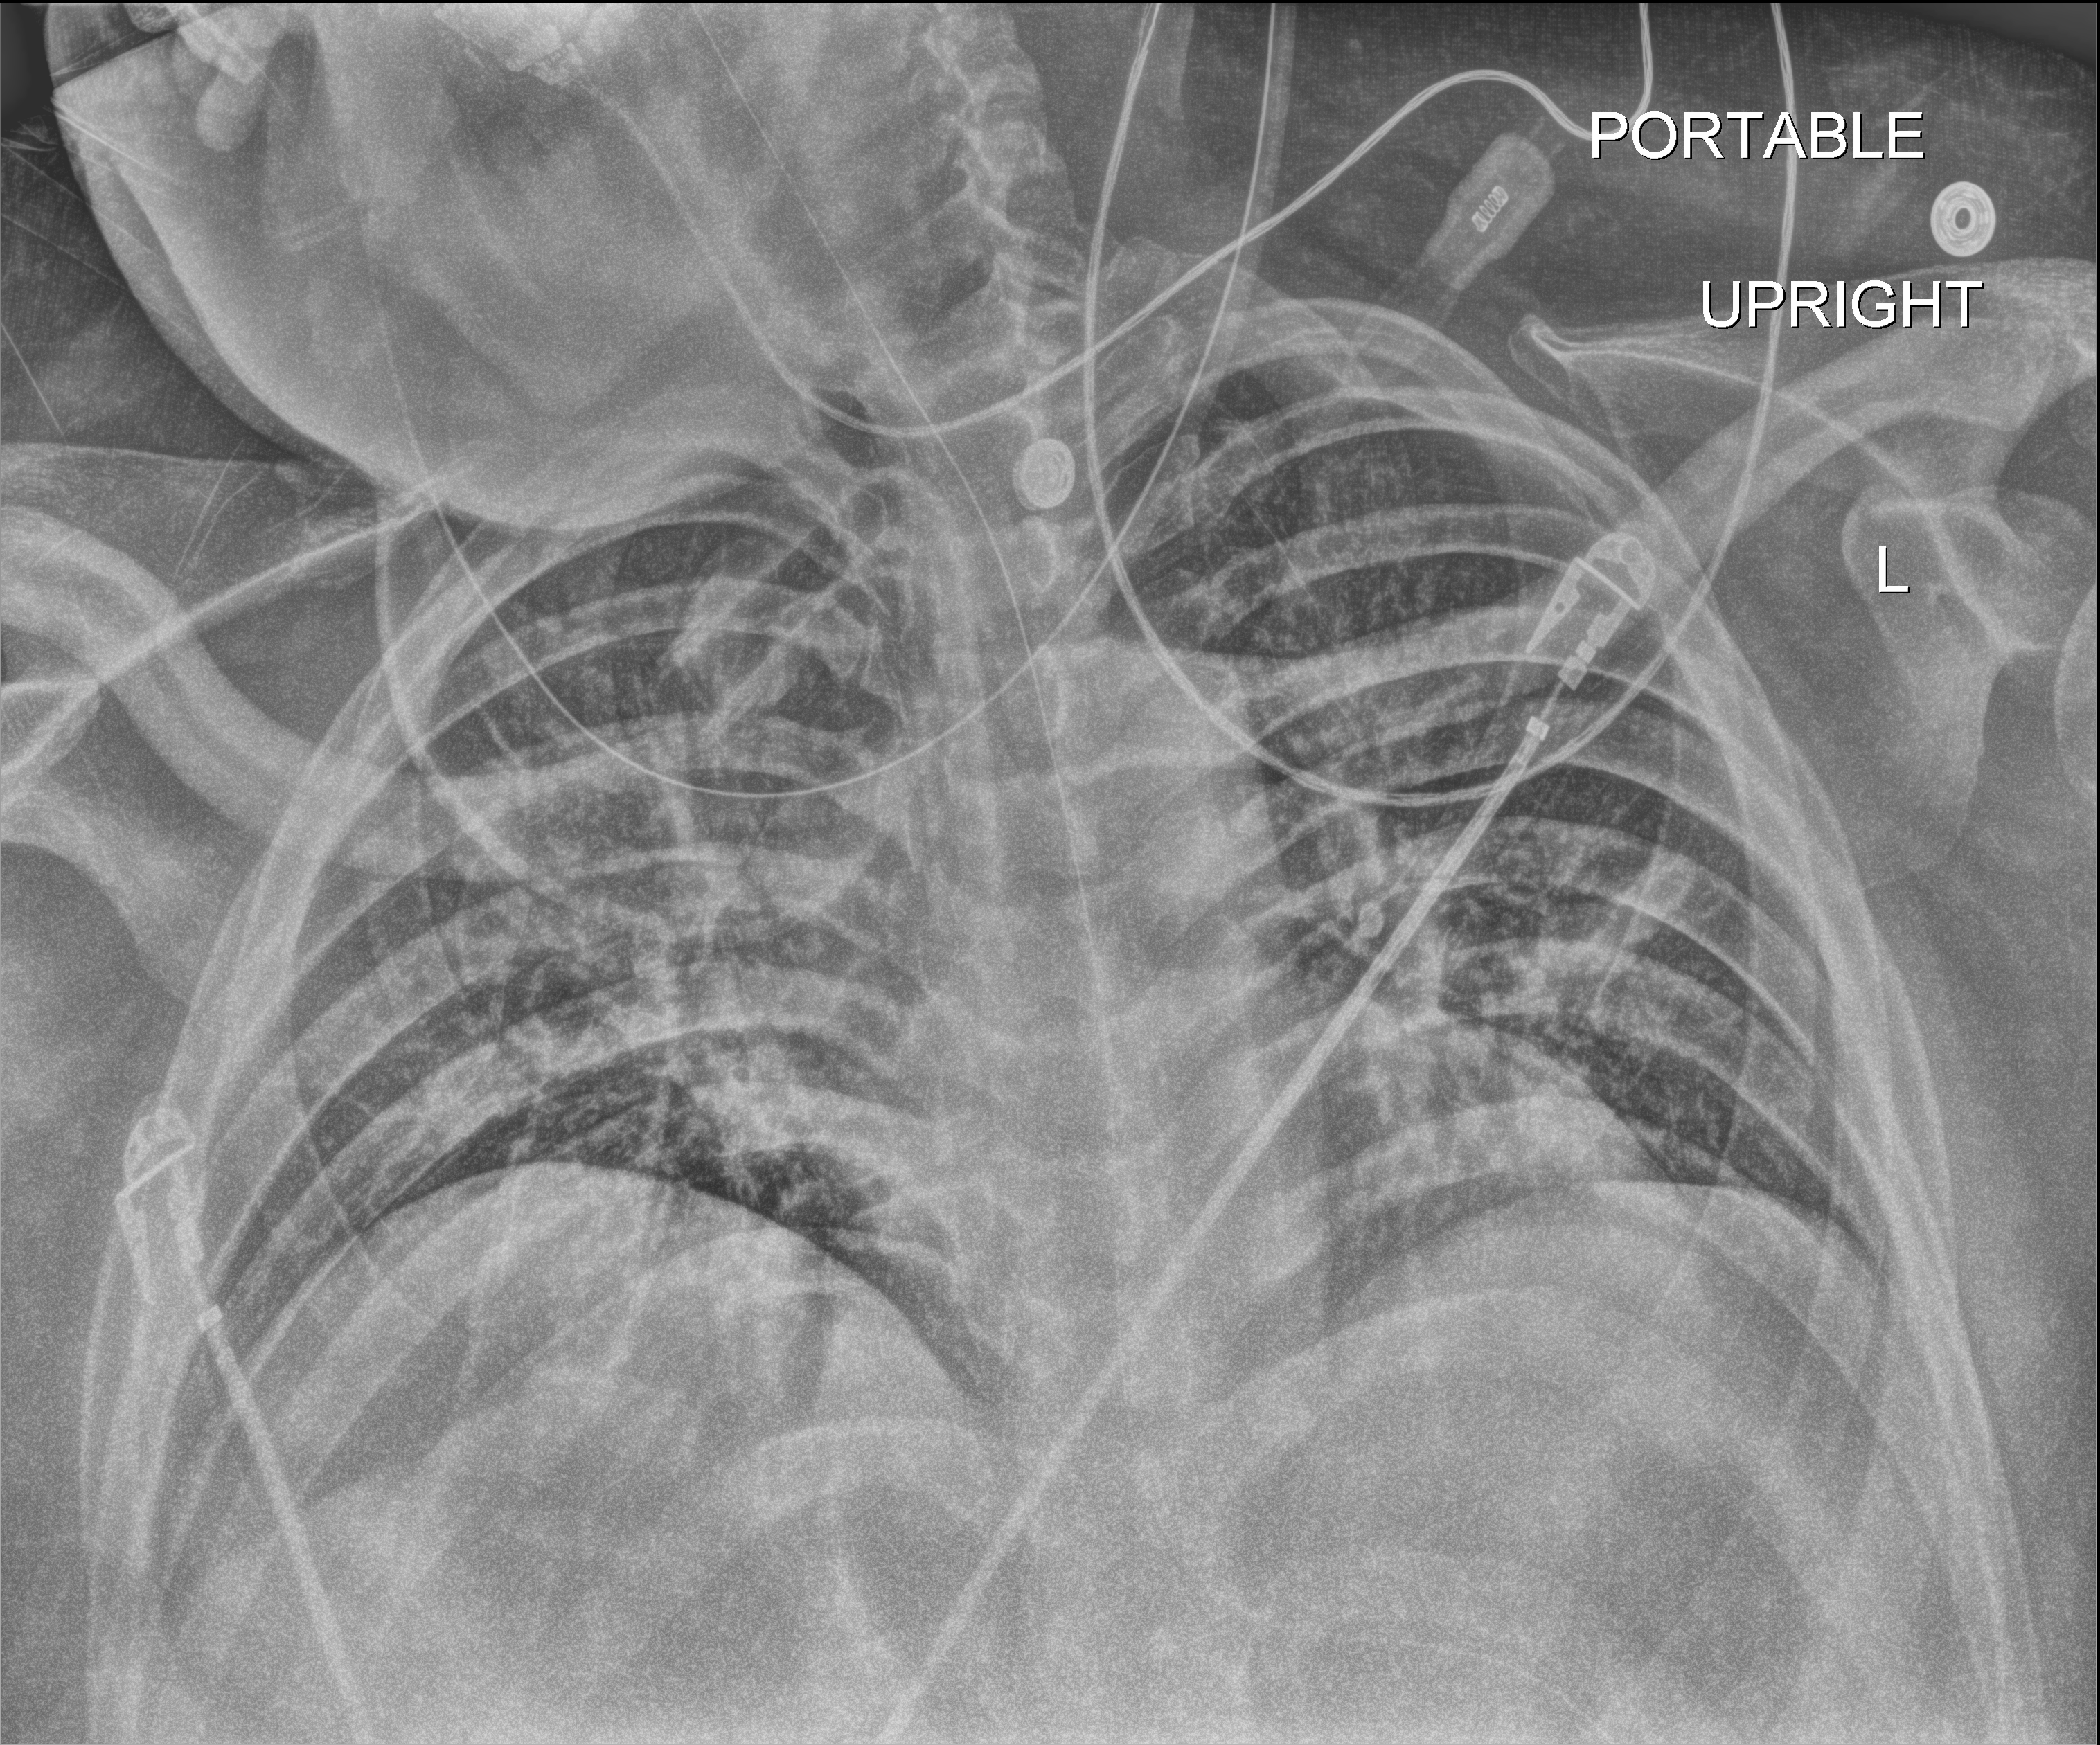
Chest X-ray (portable); anteroposterior (AP) projection. Male patient hospitalised with COVID-19, age 18–59 years.
From the hospital-stay record, not from the radiograph (when in the stay this image was taken is not recorded): other chronic lung disease (admission record): yes; COPD (admission record): yes.